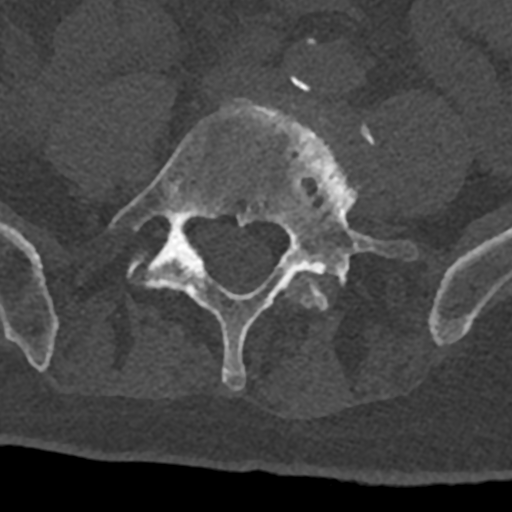
CT including the spine, one axial slice. Slice 208 of 797 in the series (ordered by position). 120 kVp. Bone window (W 1800 / L 400 HU). 0.5 mm slice thickness. 512 × 512 image matrix, field of view 160 × 160 mm. Male patient, age 74 years. Case-level facts recorded for this patient, not image findings: primary cancer: renal; vertebrae with lytic lesions (as recorded): T10, L1, L2, L3, L4, L5.
Annotated regions visible in this slice (semi-automatically segmented with operator editing):
- L4 vertebra: bounding box <284,76,375,311> (left, top, right, bottom; pixels)
- L5 vertebra: <110,98,416,391>